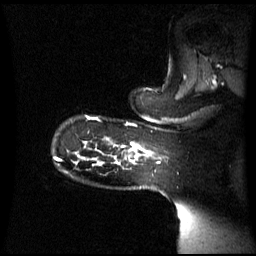
Breast MRI (dynamic contrast-enhanced), one sagittal slice; slice 50 of 60 in the series (ordered by position); dynamic contrast-enhanced series, image 2 of 3 at this slice position (ordered by acquisition); 1.5 T; TE 4.2 ms, TR 8.4 ms; 2.8 mm slice thickness; 256 × 256 image matrix, field of view 270 × 270 mm. Female patient, age 39 years. From the clinical record (not read from this slice): setting: breast cancer imaged before/during neoadjuvant chemotherapy; receptor status: triple-negative.
Structures marked on this image (semi-automatic segmentation, software-assisted and operator-edited):
- analysis volume of interest (the breast-tissue region the enhancement analysis was run in; not a lesion): bounding box [x1, y1, x2, y2] px = [101, 143, 151, 164]
- tumour enhancement mask (voxels above the 70 % enhancement threshold inside the analysis volume of interest): [134, 145, 142, 151]